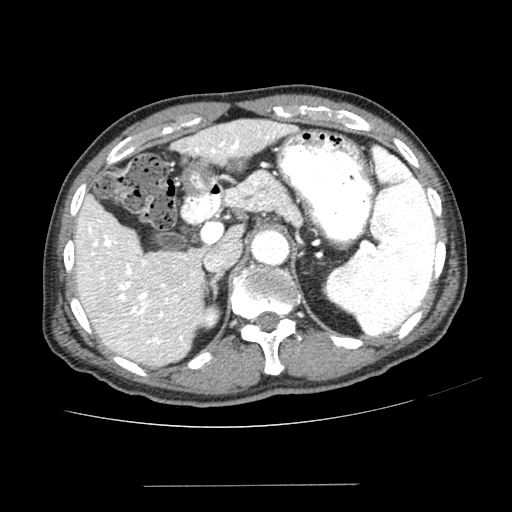
Contrast-enhanced abdominal CT (liver protocol), one axial slice; position 154 of 187 along the scan axis; one of 2 acquisitions stored at this slice position; soft-tissue window (W 400 / L 40 HU); 2.5 mm slice thickness; 512 × 512 image matrix. From the clinical record (not read from this slice): diagnosis: hepatocellular carcinoma (patient treated with transarterial chemoembolisation; whether this scan precedes or follows treatment is not stated here); TNM stage (as recorded): Stage-I; Child-Pugh class: A; tumour nodularity: uninodular; tumour size: 1.6 cm.
Outlined on this slice (semi-automatic segmentation, software-assisted and operator-edited):
- liver parenchyma outside the tumour (the mass and vessels are separate outlines, so this box may not span the whole liver): box from (x=76, y=120) to (x=296, y=366) px
- liver vessels: (x=84, y=127)–(x=280, y=345)